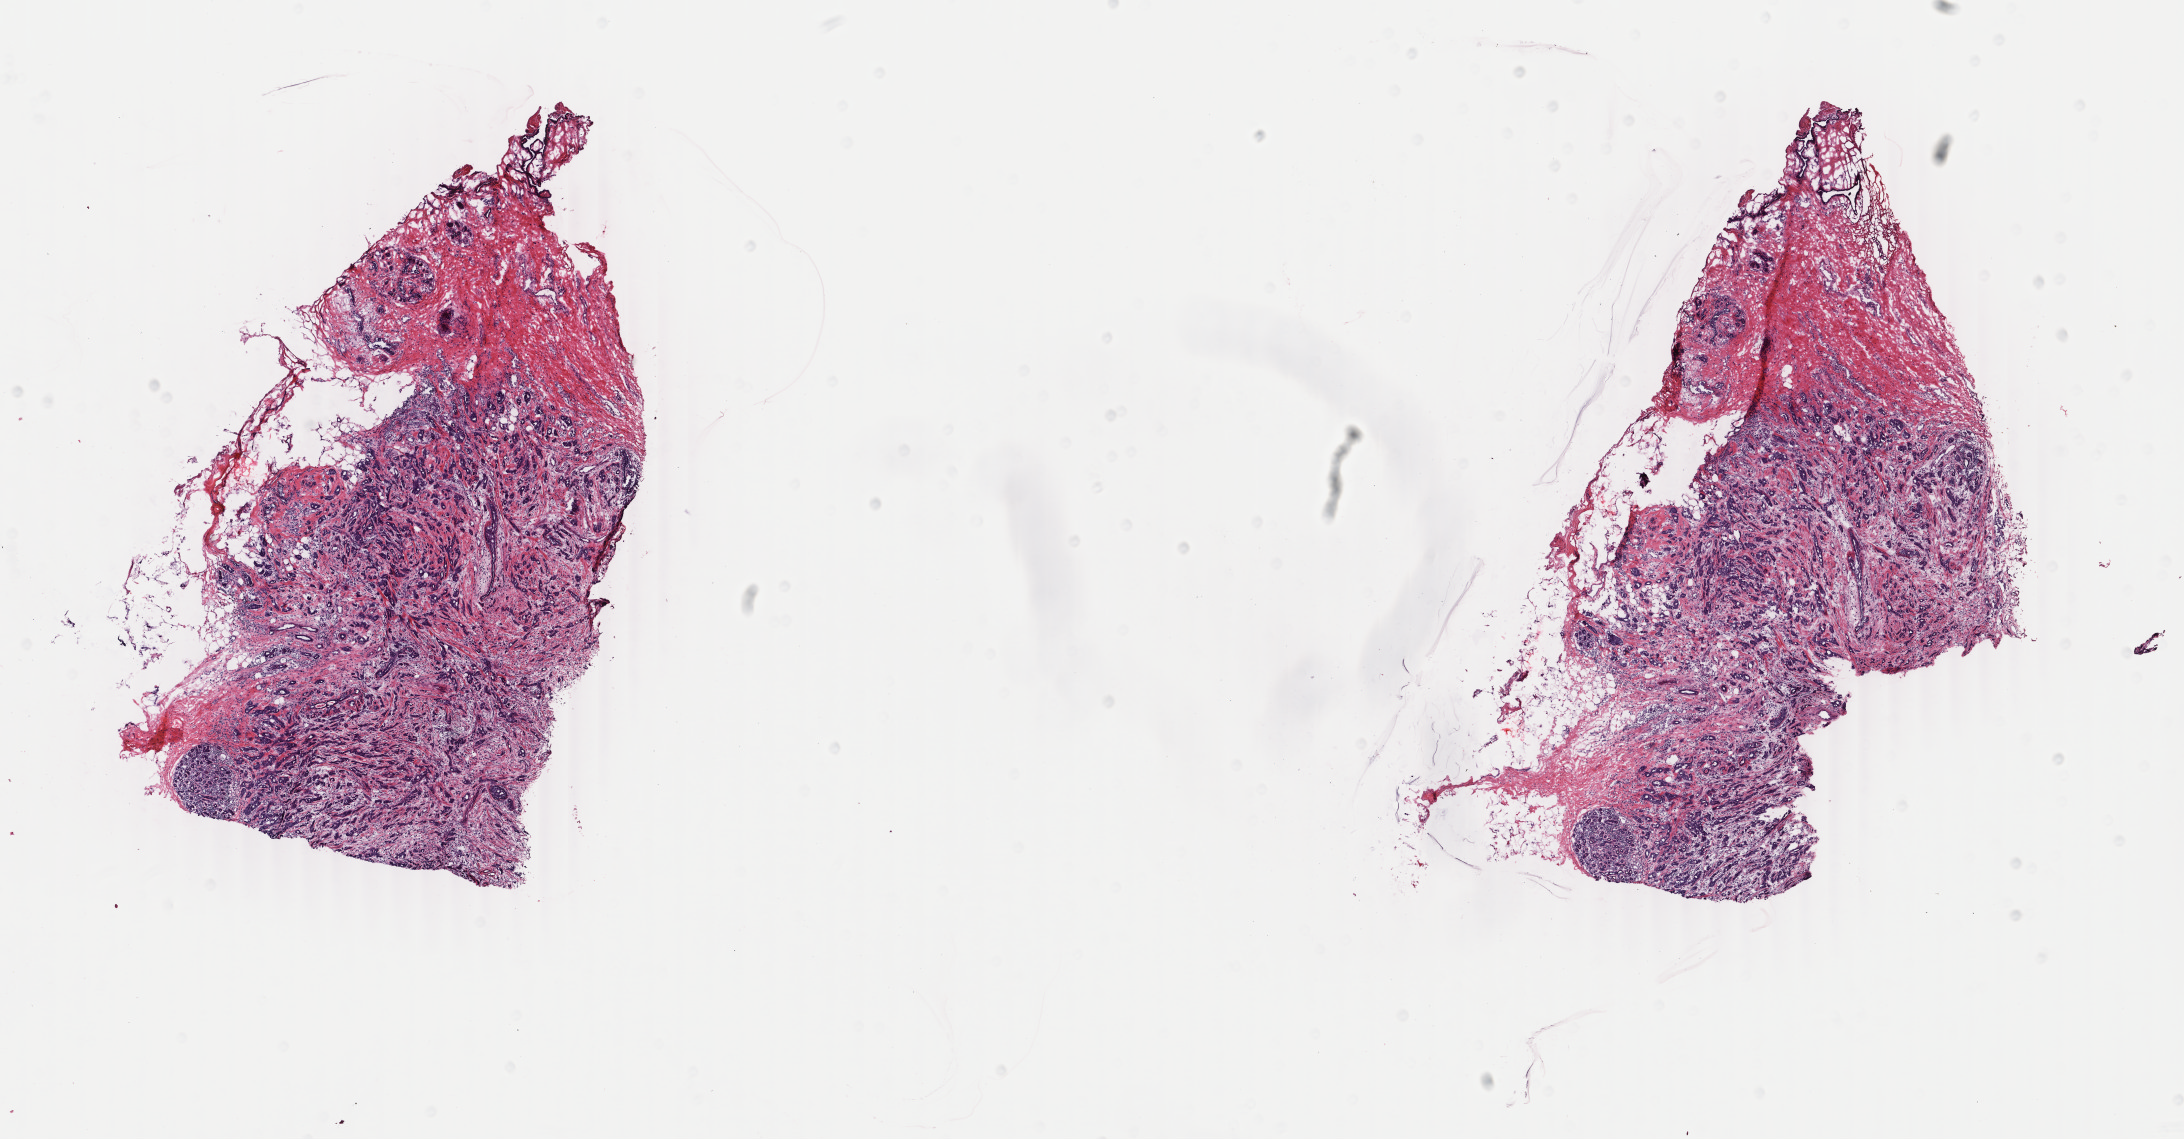
Whole-slide histology image, H&E — a low-resolution overview of the entire scanned area, about 17.4 x 9.1 mm (slide scanned at 40x), frozen section from the top of the tissue portion, sample: primary tumour, breast. Female, age 41 years at initial diagnosis. Slide review estimates, as recorded: tumour cells 60%, tumour nuclei 60%, normal cells 0%, stromal cells 30%, necrosis 10%. Inflammatory infiltration, as recorded: lymphocyte infiltration 10%, monocyte infiltration 30%, neutrophil infiltration 20%.
AJCC pathologic stage: IIB (6th edition). TNM: T2 N1a M0. Histologic diagnosis: Infiltrating duct carcinoma, NOS.